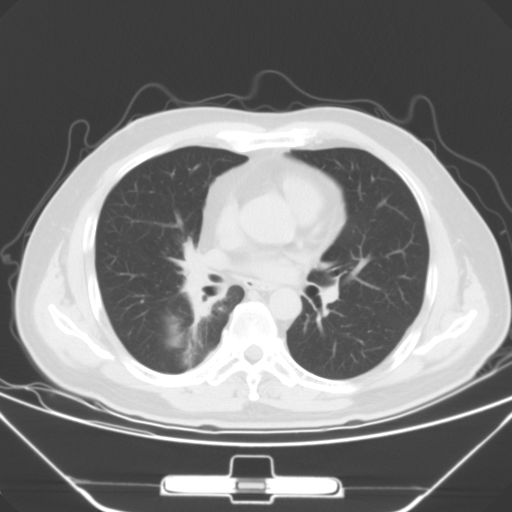
Chest CT, one axial slice. Position 28 of 56 along the scan axis. 120 kVp. Lung window (W 1500 / L -600 HU). 5 mm slice thickness. 512 × 512 image matrix, field of view 371 × 371 mm. Male patient, age 48 years. Case-level facts recorded for this patient, not image findings: clinical TNM (as recorded): T1a N1 M1c.
Annotated regions visible in this slice (bounding box drawn by a radiologist):
- lung tumour (recorded histology: adenocarcinoma): bounding box (x1, y1, x2, y2) in pixels: (174, 245, 222, 326)